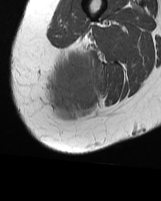
MRI of an extremity soft-tissue mass, one axial slice. Slice 15 of 70 in the series (ordered by position). MR volume resampled by the dataset authors to the PET/CT grid (not the native acquisition matrix). 3.27 mm slice thickness. 161 × 201 image matrix, field of view 157 × 196 mm. Female patient. From the clinical record (not read from this slice): histological type: synovial sarcoma; grade: intermediate; site of the primary tumour: right buttock.
Structures marked on this image (expert contour drawn on MRI and transferred to this co-registered scan by the dataset authors):
- gross tumour volume including surrounding oedema: box from (x=47, y=47) to (x=100, y=116) px
- gross tumour volume (mass): (x=49, y=56)–(x=100, y=112)